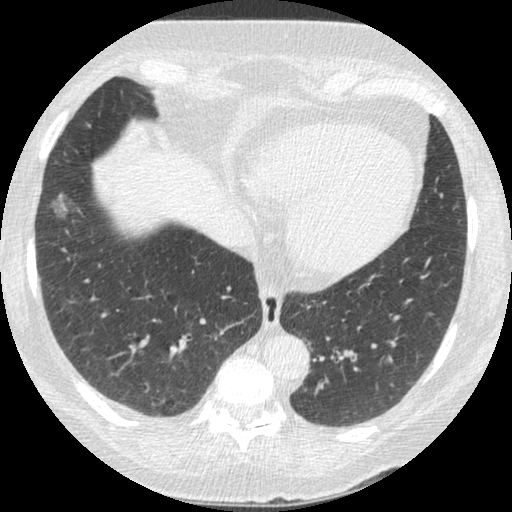
Low-dose screening chest CT, one axial slice; position 88 of 245 along the scan axis; reconstruction kernel STANDARD; lung window (W 1500 / L -600 HU); 512 × 512 image matrix, field of view 310 × 310 mm.
Annotated regions visible in this slice (outlined manually by an expert reader):
- lesion 1 (tumor, lower lobe of right lung): bounding box (x1, y1, x2, y2) in pixels: (52, 194, 70, 218)